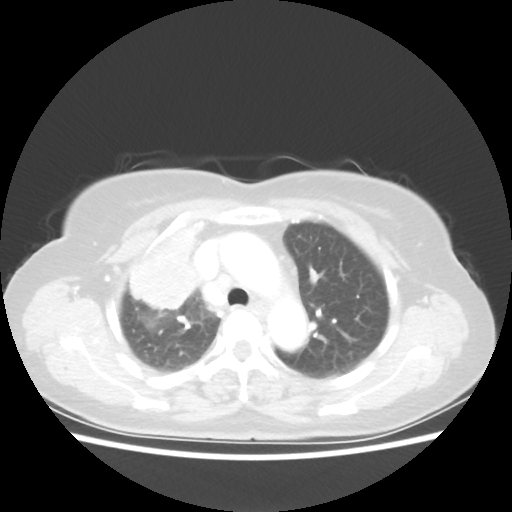
Chest CT, one axial slice; position 39 of 55 along the scan axis; reconstruction kernel STANDARD; lung window (W 1500 / L -600 HU); 5 mm slice thickness; 512 × 512 image matrix, field of view 337 × 337 mm. Female patient, age 62 years. Case-level facts recorded for this patient, not image findings: clinical TNM (as recorded): T4 N3 M0.
Outlined on this slice (rectangle marked by the reading radiologist):
- lung tumour (recorded histology: squamous cell carcinoma): bounding box [x1, y1, x2, y2] px = [115, 216, 222, 311]